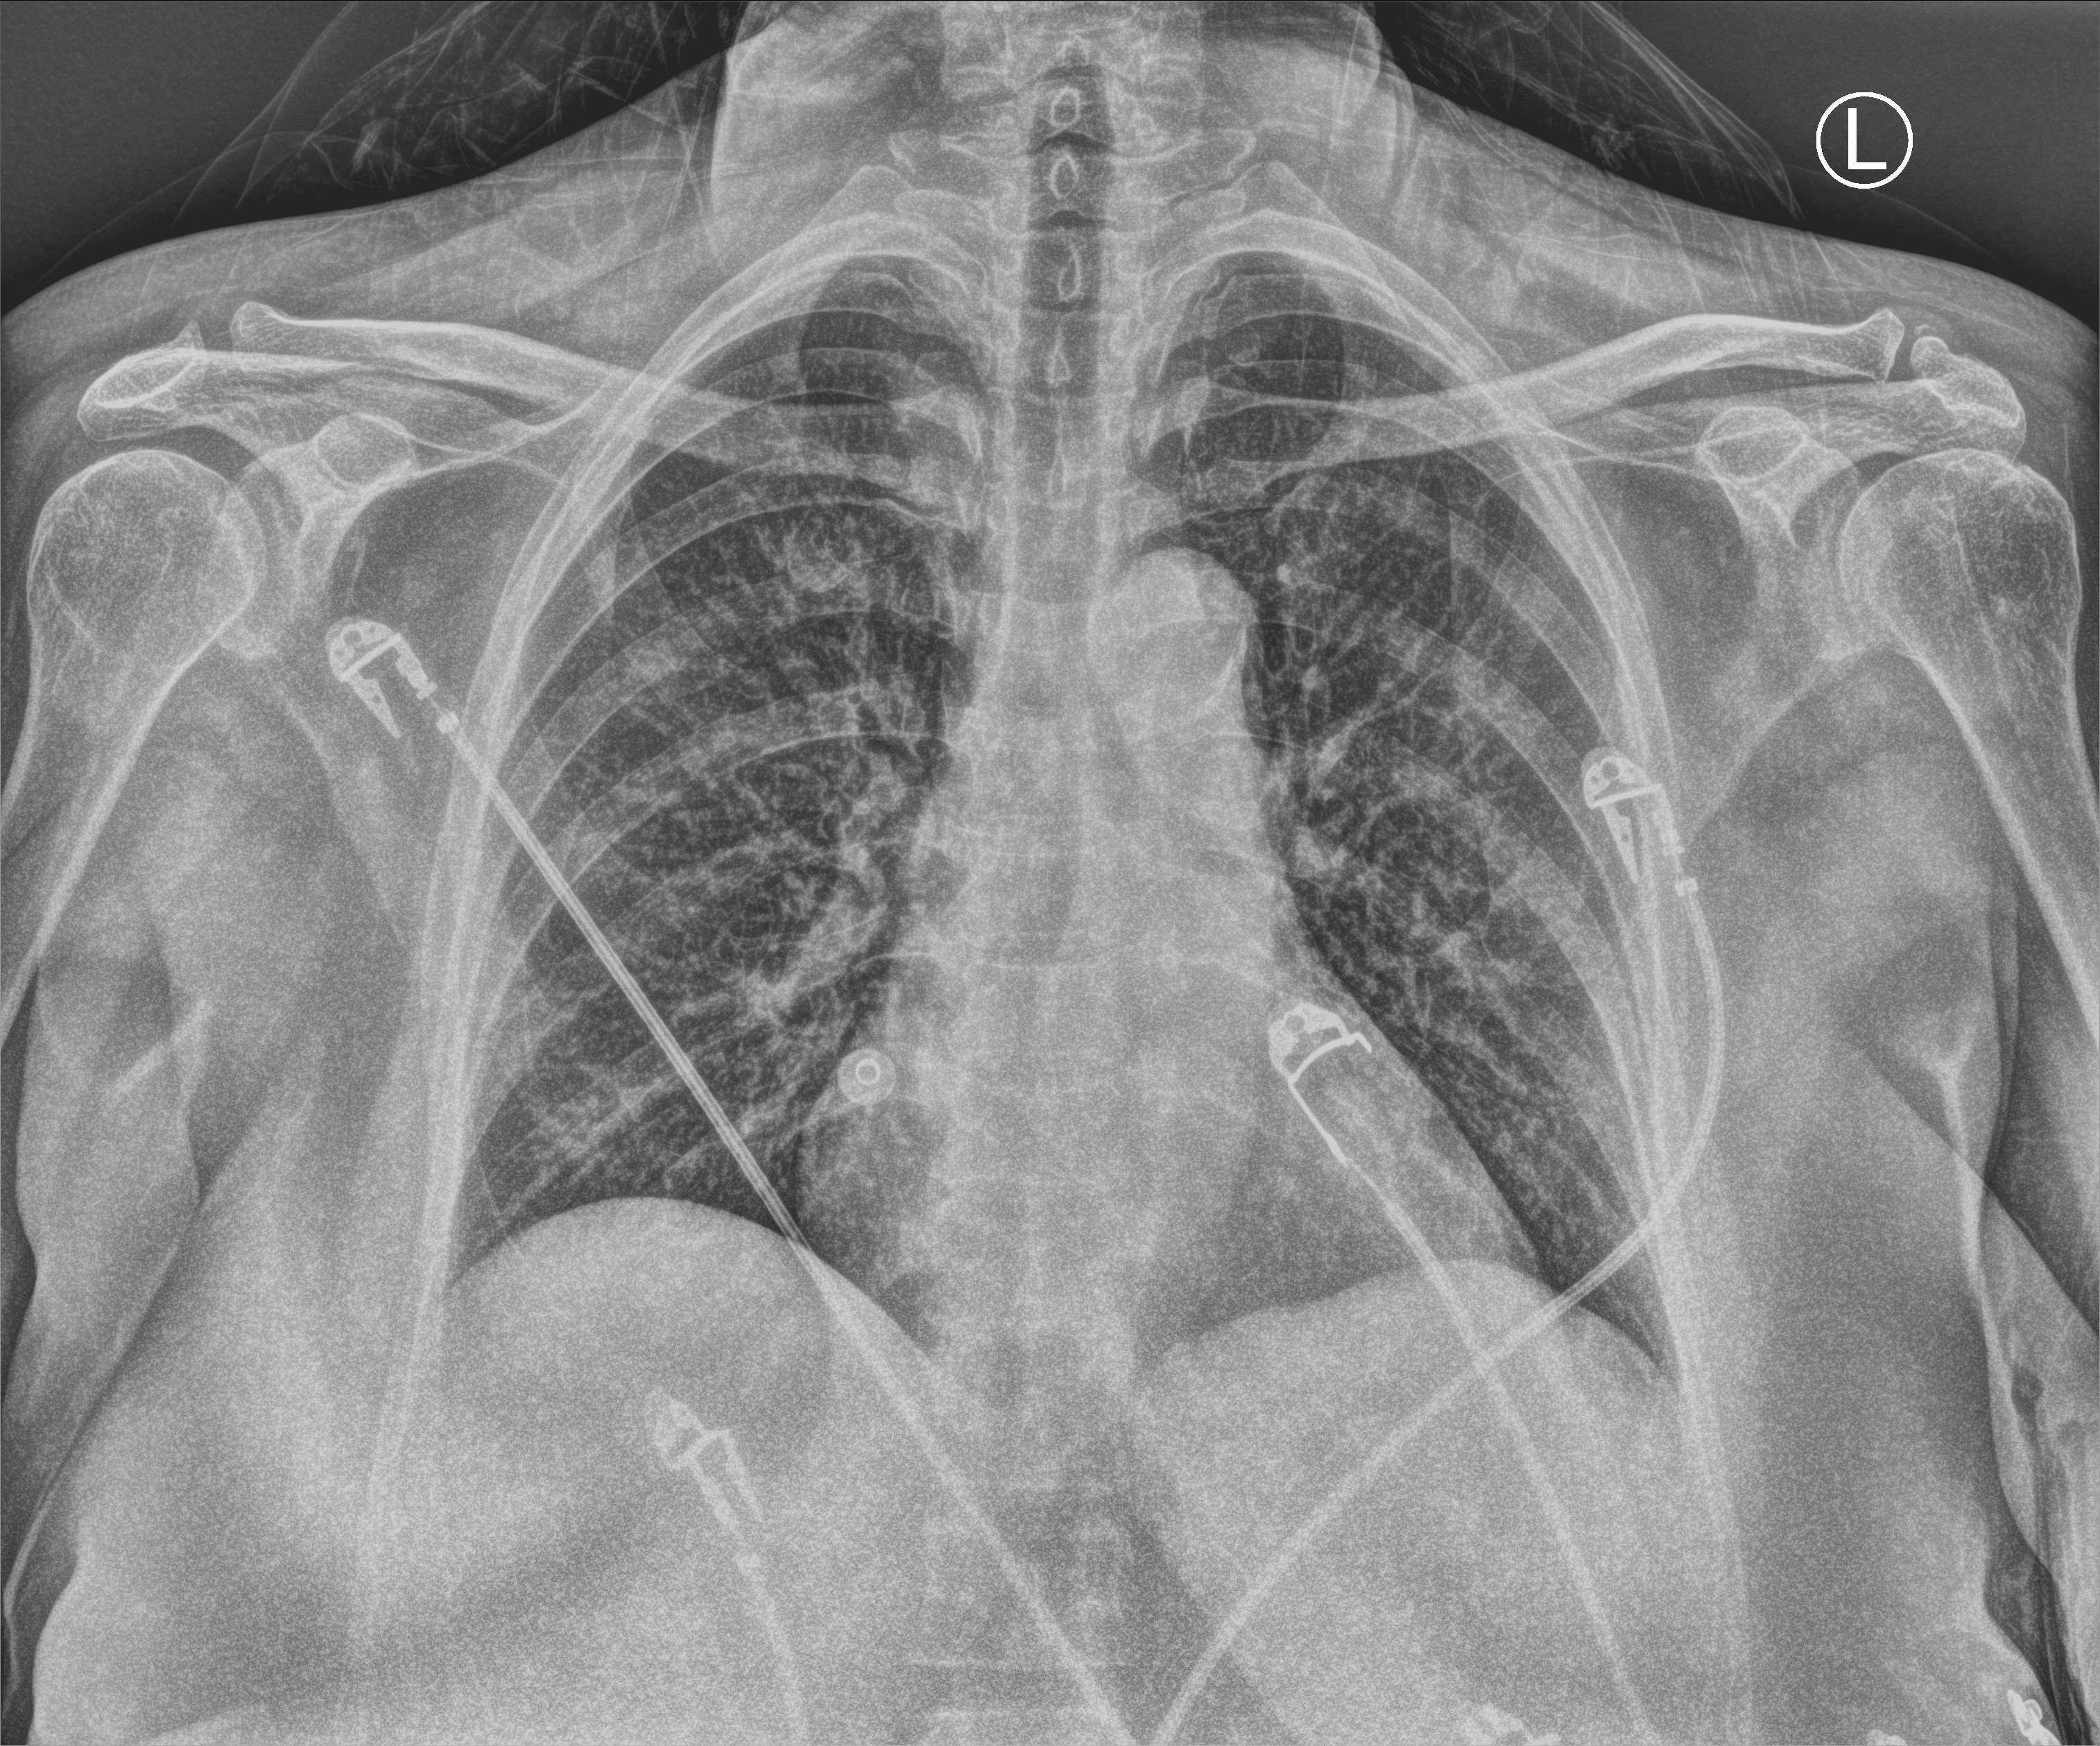
Bedside chest radiograph (computed radiography), anteroposterior (AP) projection. Female patient hospitalised with COVID-19, age 60–74 years.
Admission-level facts for this patient (not findings on this image; timing relative to this image not recorded): smoking status (admission record): never; length of hospital stay: 3 days; admitted to intensive care during this hospital stay: no.